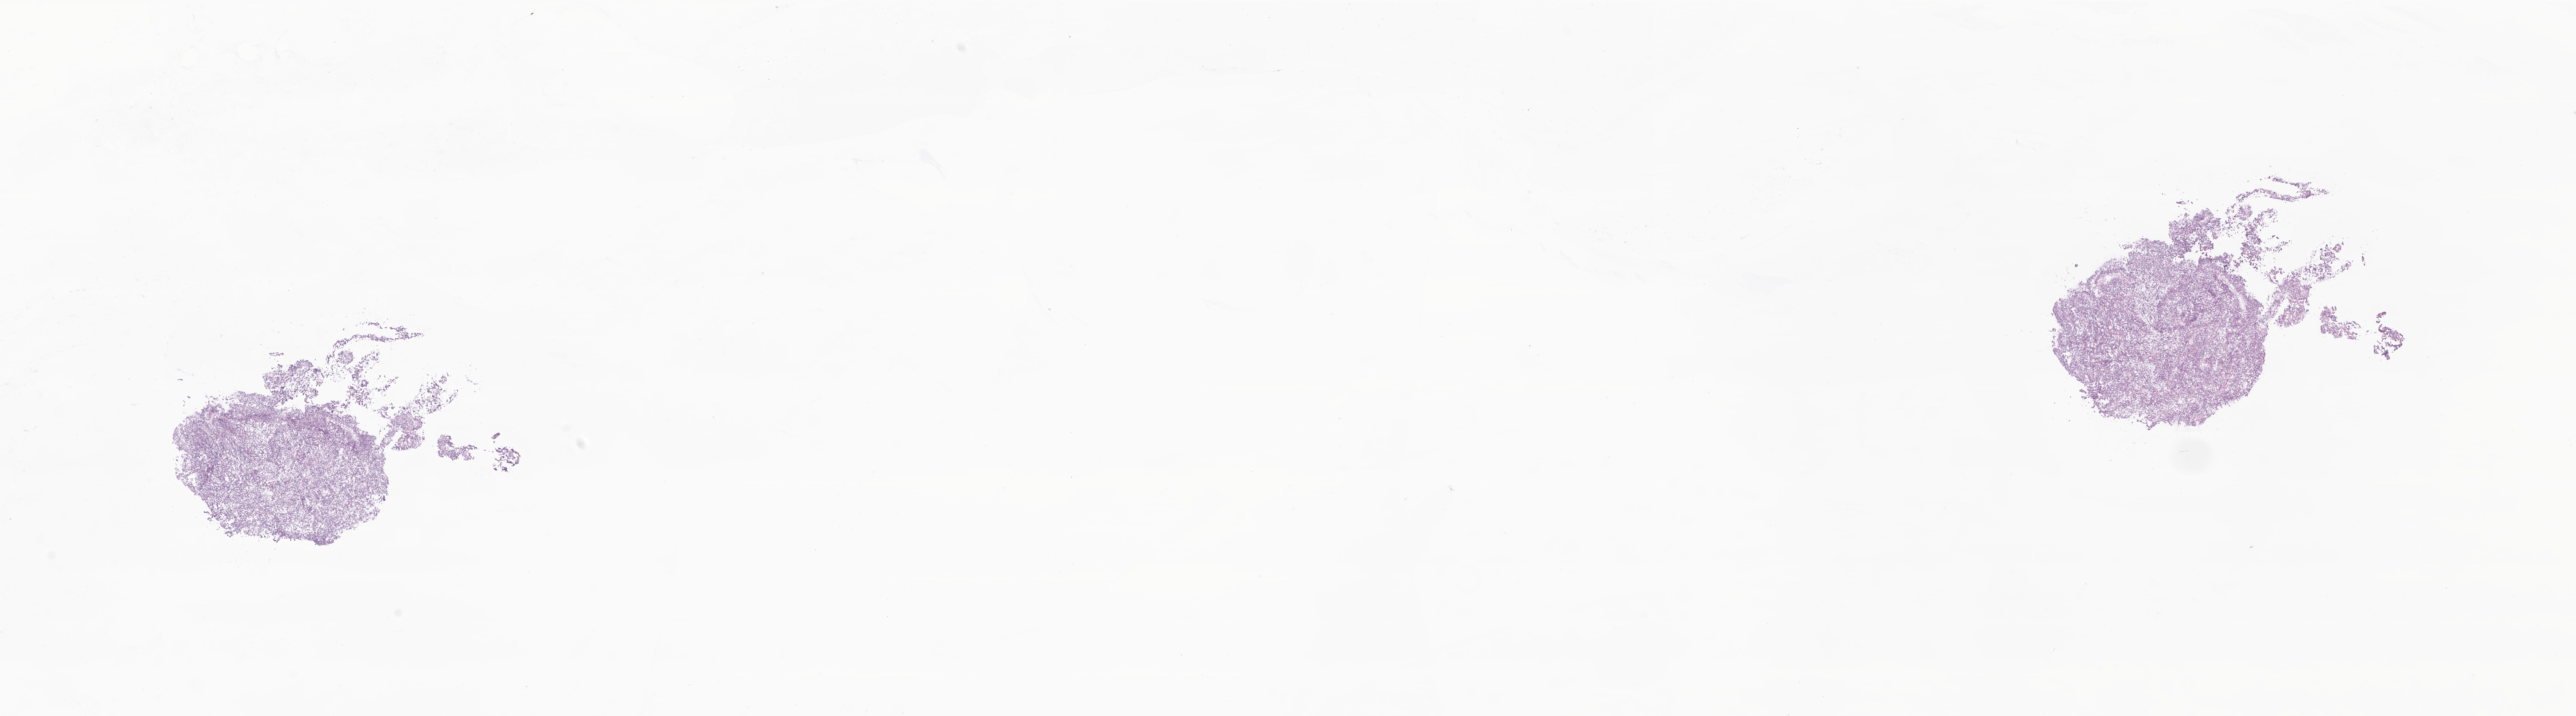
Haematoxylin and eosin whole-slide image of tumor tissue from the cerebral ventricle, whole scanned area (about 28.8 x 8.0 mm) shown as a low-resolution overview, frozen section. Female patient, age 65 months (5 years 5 months).
Diagnosis (ICD-O-3 morphology term): Choroid plexus carcinoma.